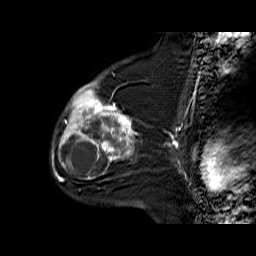
Breast MRI (dynamic contrast-enhanced), one sagittal slice. Position 42 of 60 along the scan axis. Dynamic contrast-enhanced series, time point 2 of 6 at this slice position (early post-contrast). 1.5 T. TE 6.3 ms, TR 32.9 ms. 4 mm slice thickness. 256 × 256 image matrix. Female patient. Case-level facts recorded for this patient, not image findings: setting: breast cancer imaged before/during neoadjuvant chemotherapy; receptor status: triple-negative.
Annotated regions visible in this slice (semi-automatic segmentation, software-assisted and operator-edited):
- analysis volume of interest (the breast-tissue region the enhancement analysis was run in; not a lesion): box from (x=55, y=76) to (x=137, y=170) px
- tumour enhancement mask (voxels above the 100 % enhancement threshold inside the analysis volume of interest): (x=59, y=82)–(x=134, y=165)